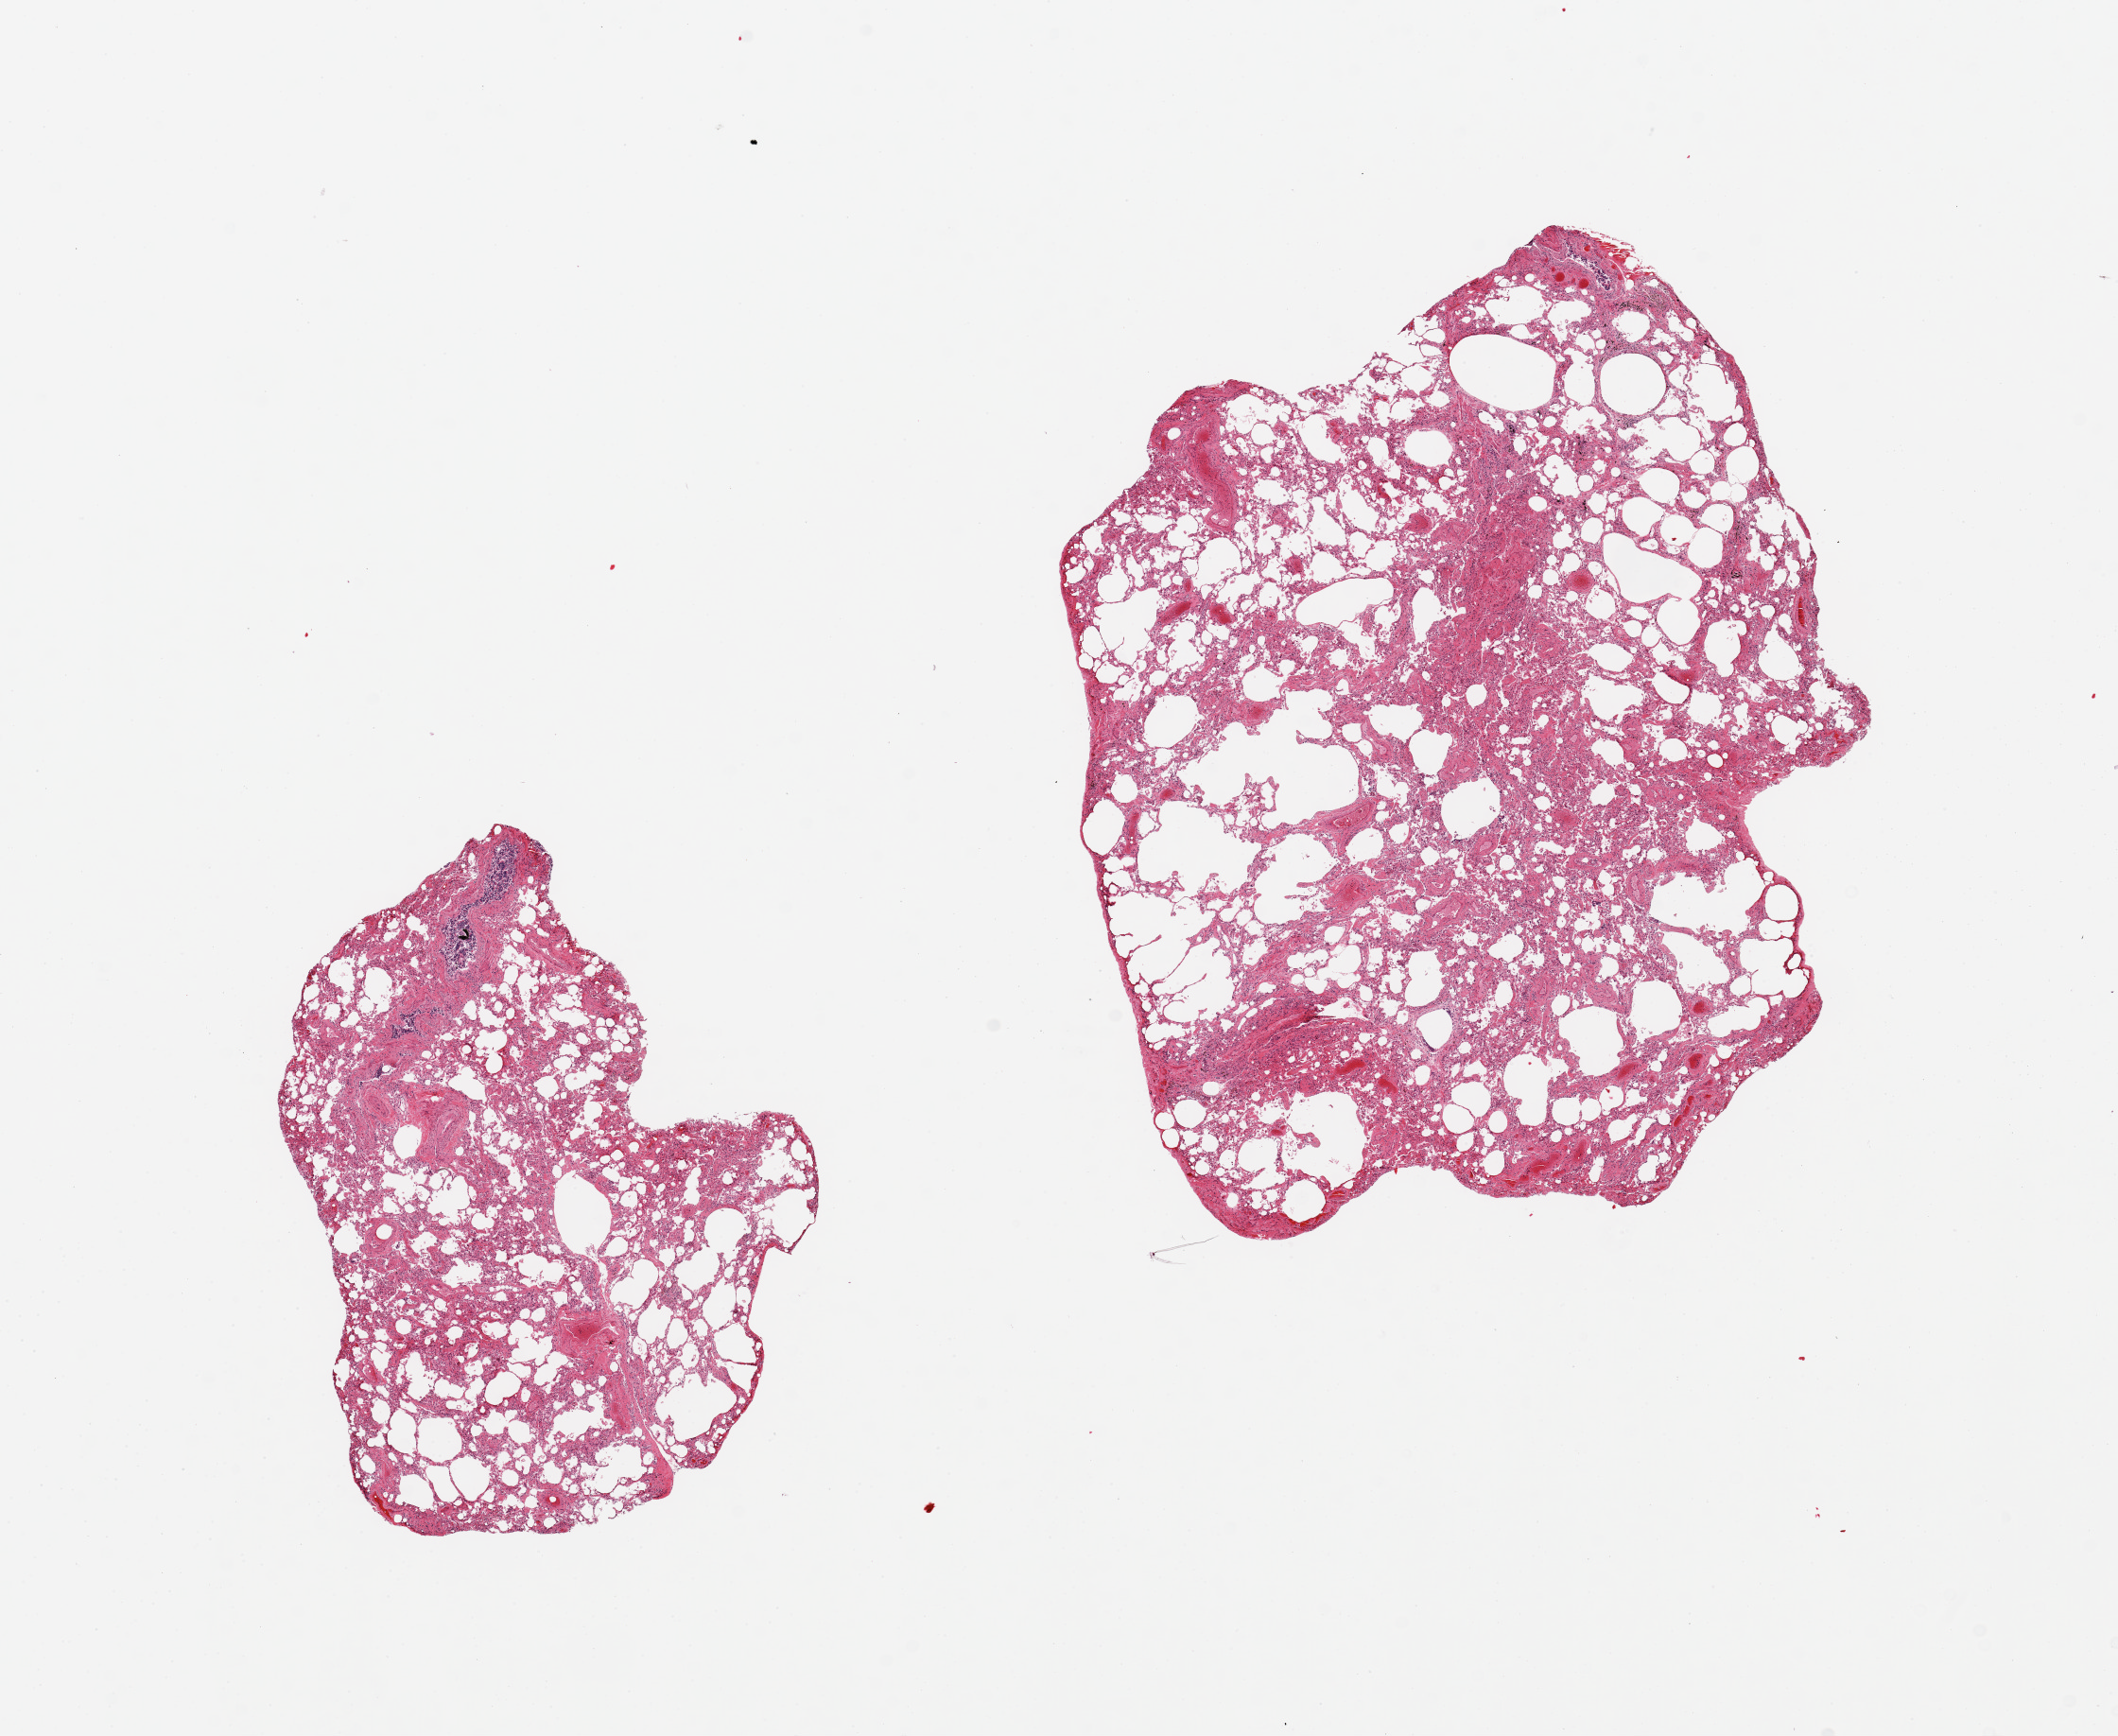
Whole-slide image, H&E stain, brightfield, whole scanned area (about 17.7 x 14.5 mm, acquisition: 20x scan) shown as a low-resolution overview; PAXgene-fixed paraffin-embedded (PFPE) section; section of lung (target tissue); tissue donor sample.
Review note (as recorded): 2 pieces, congestion/edema, emphysematous changes, moderate-marked autolysis.